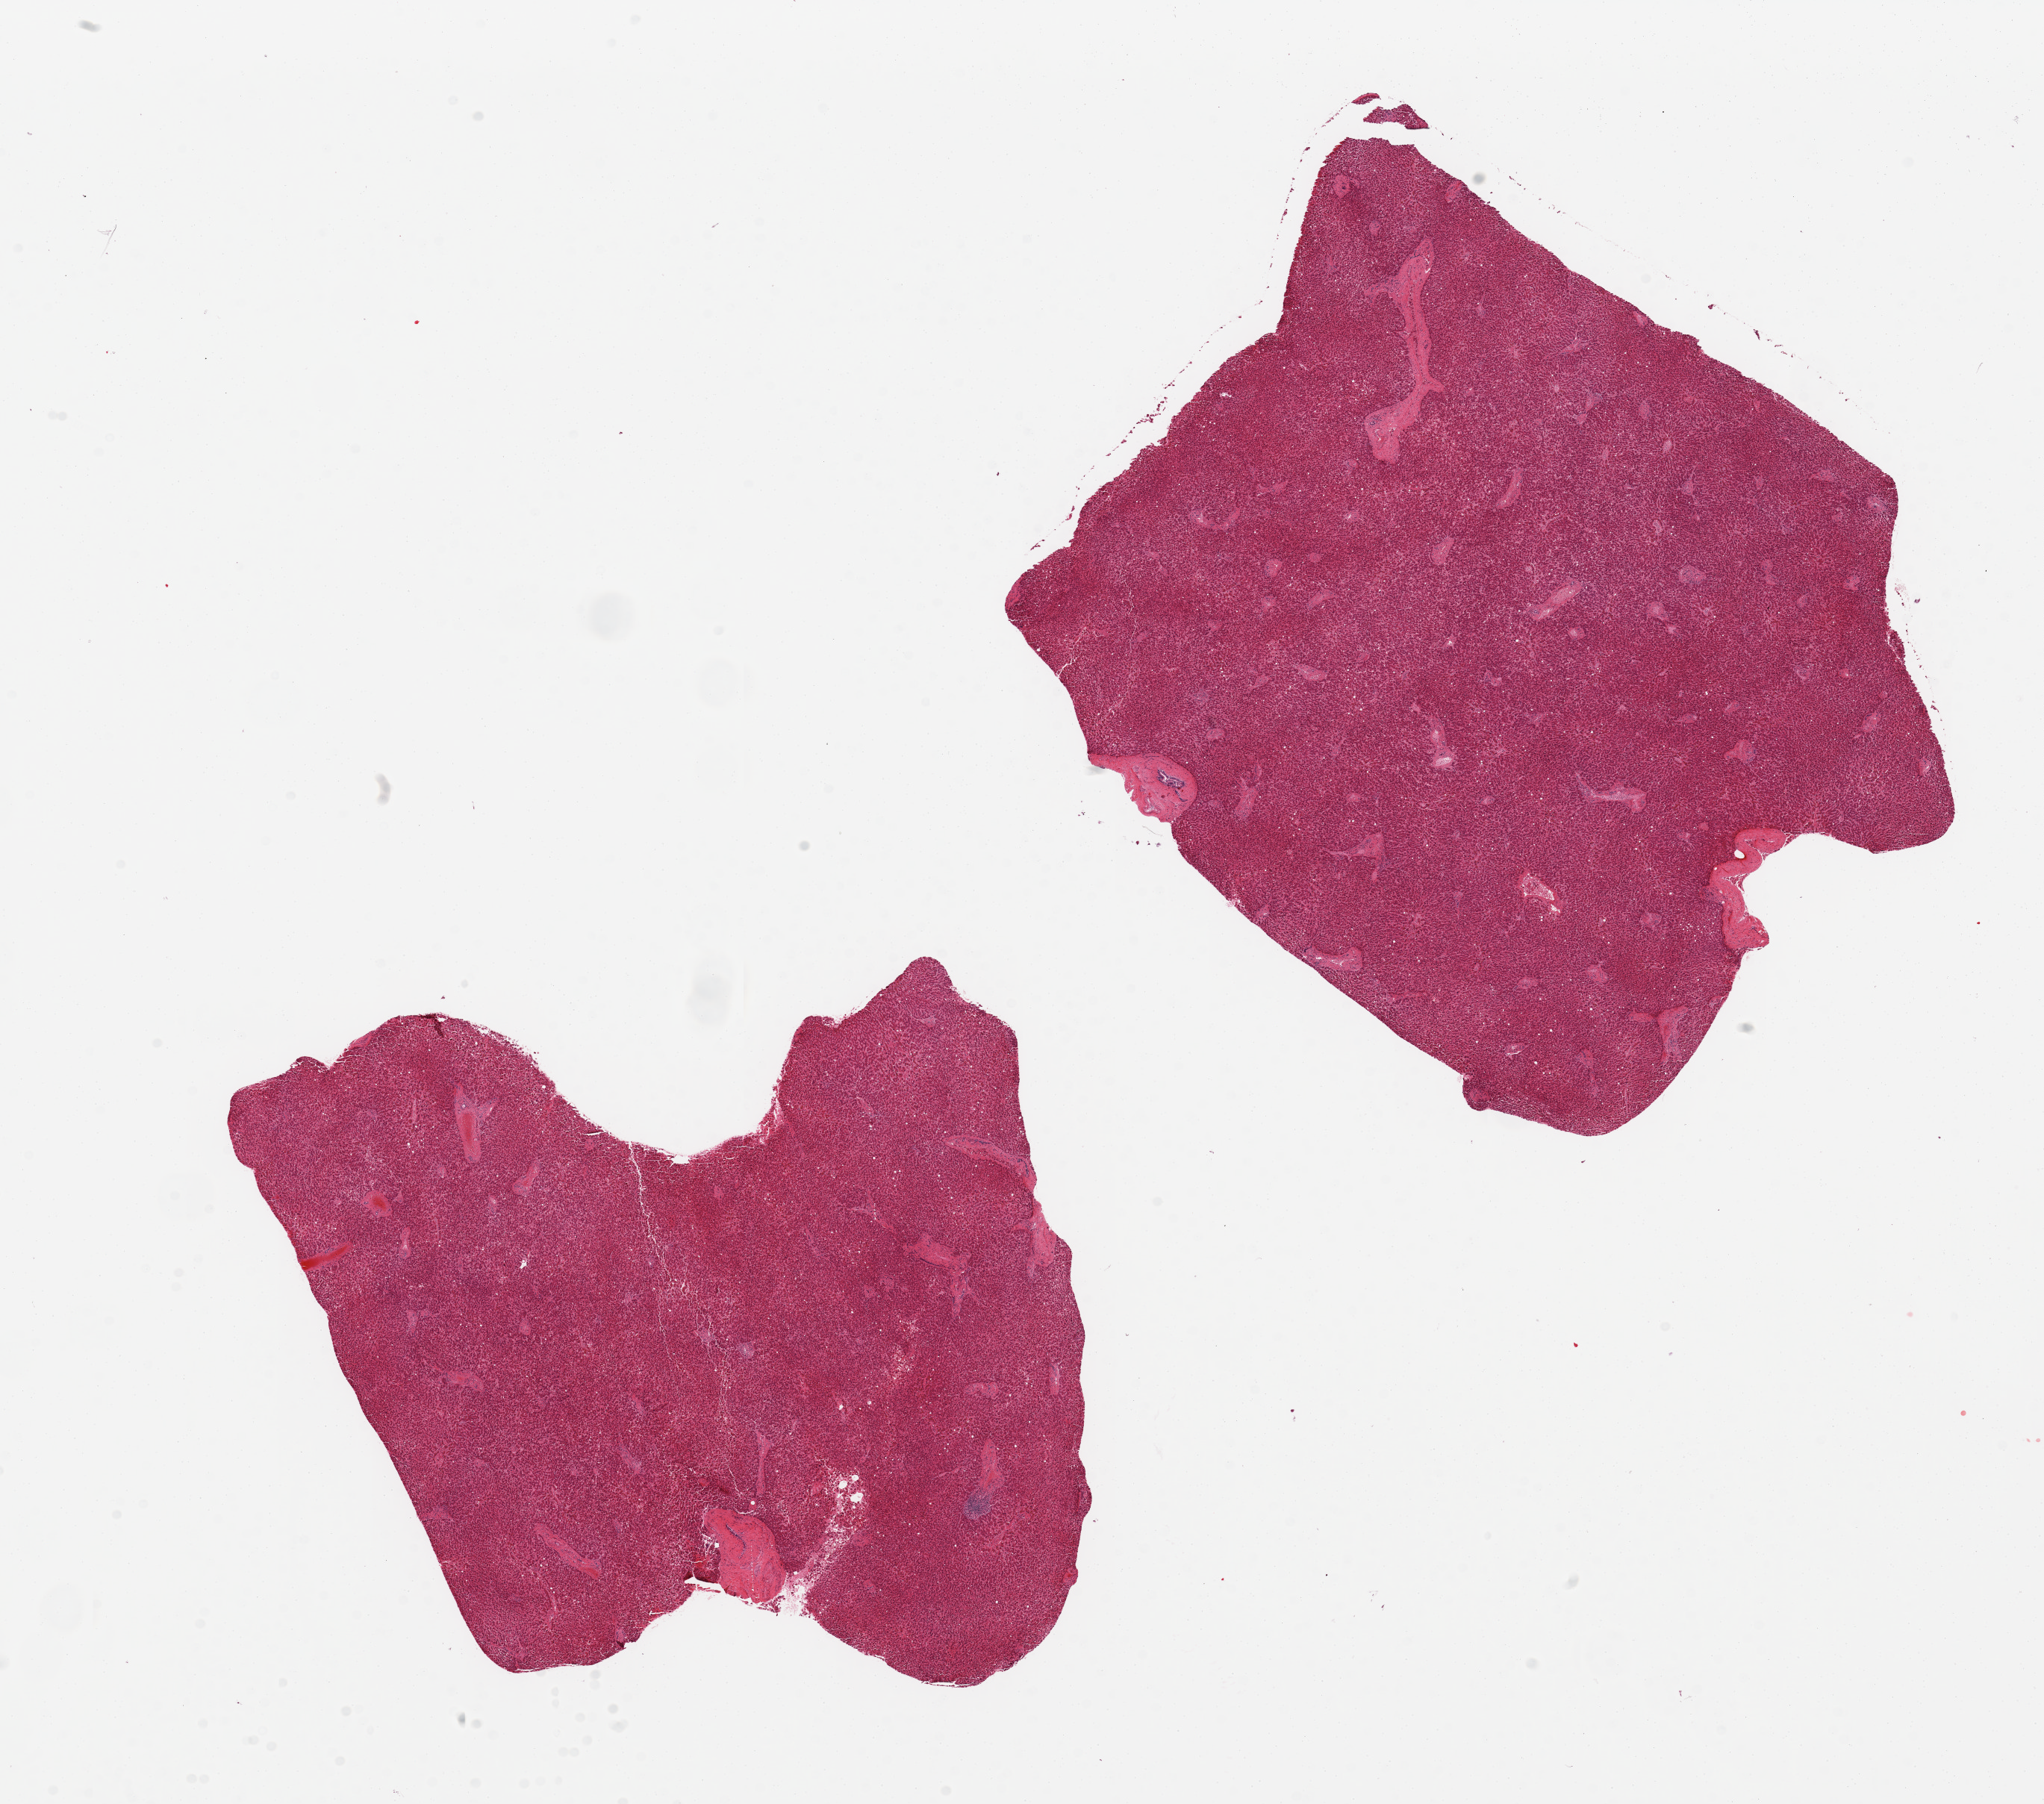
Hematoxylin and eosin (H&E) whole-slide image, brightfield — low-resolution overview of the scanned area, about 21.7 x 19.1 mm. PAXgene-fixed paraffin-embedded (PFPE) section. Sampled site (target tissue): liver. Donor tissue sample. Male donor.
- reviewer comment on this tissue sample: 2 pieces